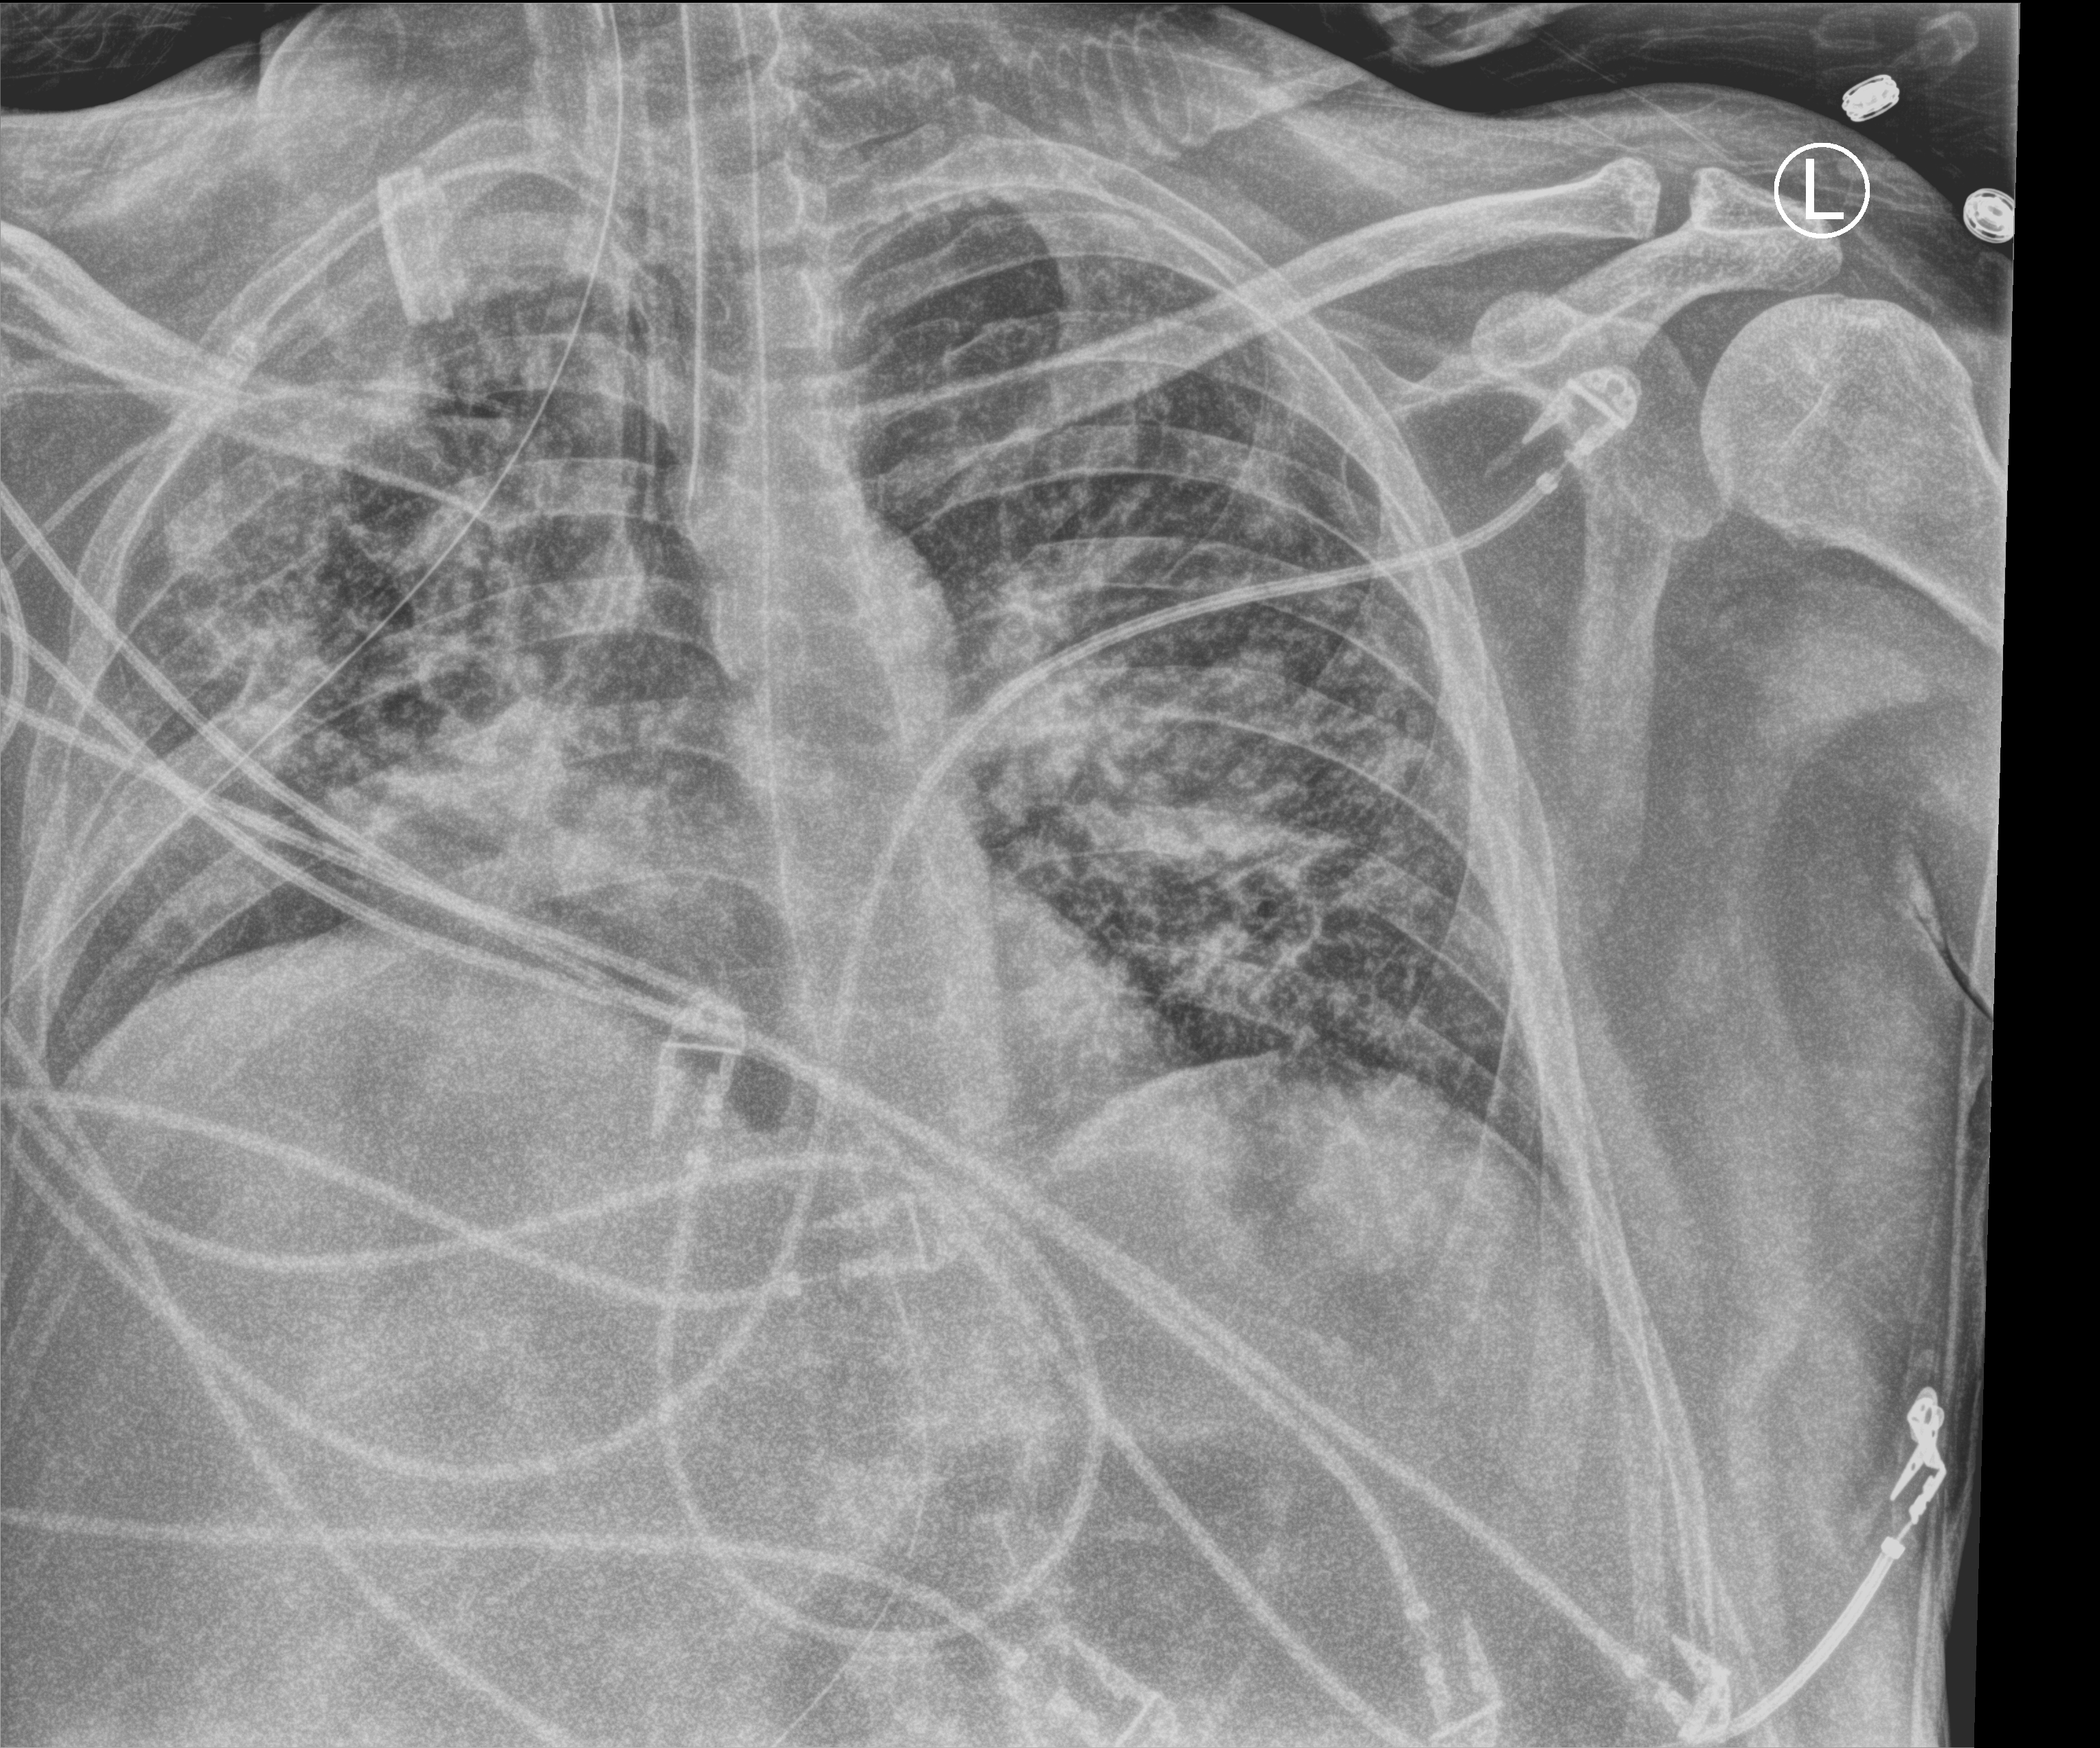
Bedside chest radiograph (computed radiography). Adult patient hospitalised with COVID-19, age 18–59 years.
Hospital-stay facts (about this admission, not read from this image; timing relative to this image not recorded): length of hospital stay: 50 days; mechanically ventilated during this hospital stay: yes; smoking status (admission record): never.